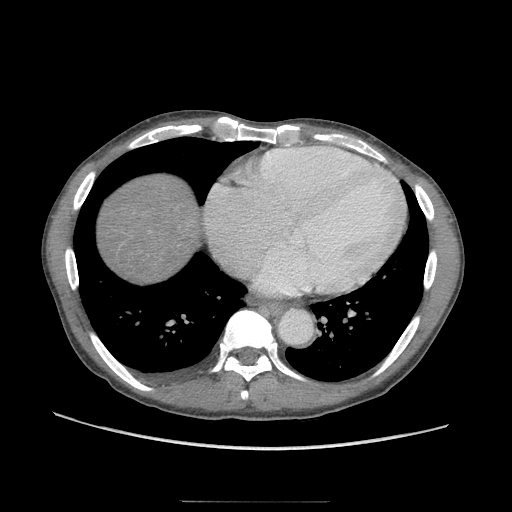
Contrast-enhanced abdominal CT (liver protocol), one axial slice; position 97 of 103 along the scan axis; soft-tissue window (W 400 / L 40 HU); 512 × 512 image matrix, field of view 380 × 380 mm. From the clinical record (not read from this slice): diagnosis: hepatocellular carcinoma (patient treated with transarterial chemoembolisation; whether this scan precedes or follows treatment is not stated here); TNM stage (as recorded): Stage-IIIA; Child-Pugh class: A.
Structures marked on this image (semi-automatically segmented with operator editing):
- abdominal aorta: bounding box <278,308,311,344> (left, top, right, bottom; pixels)
- liver parenchyma outside the tumour (the mass and vessels are separate outlines, so this box may not span the whole liver): <102,178,196,275>